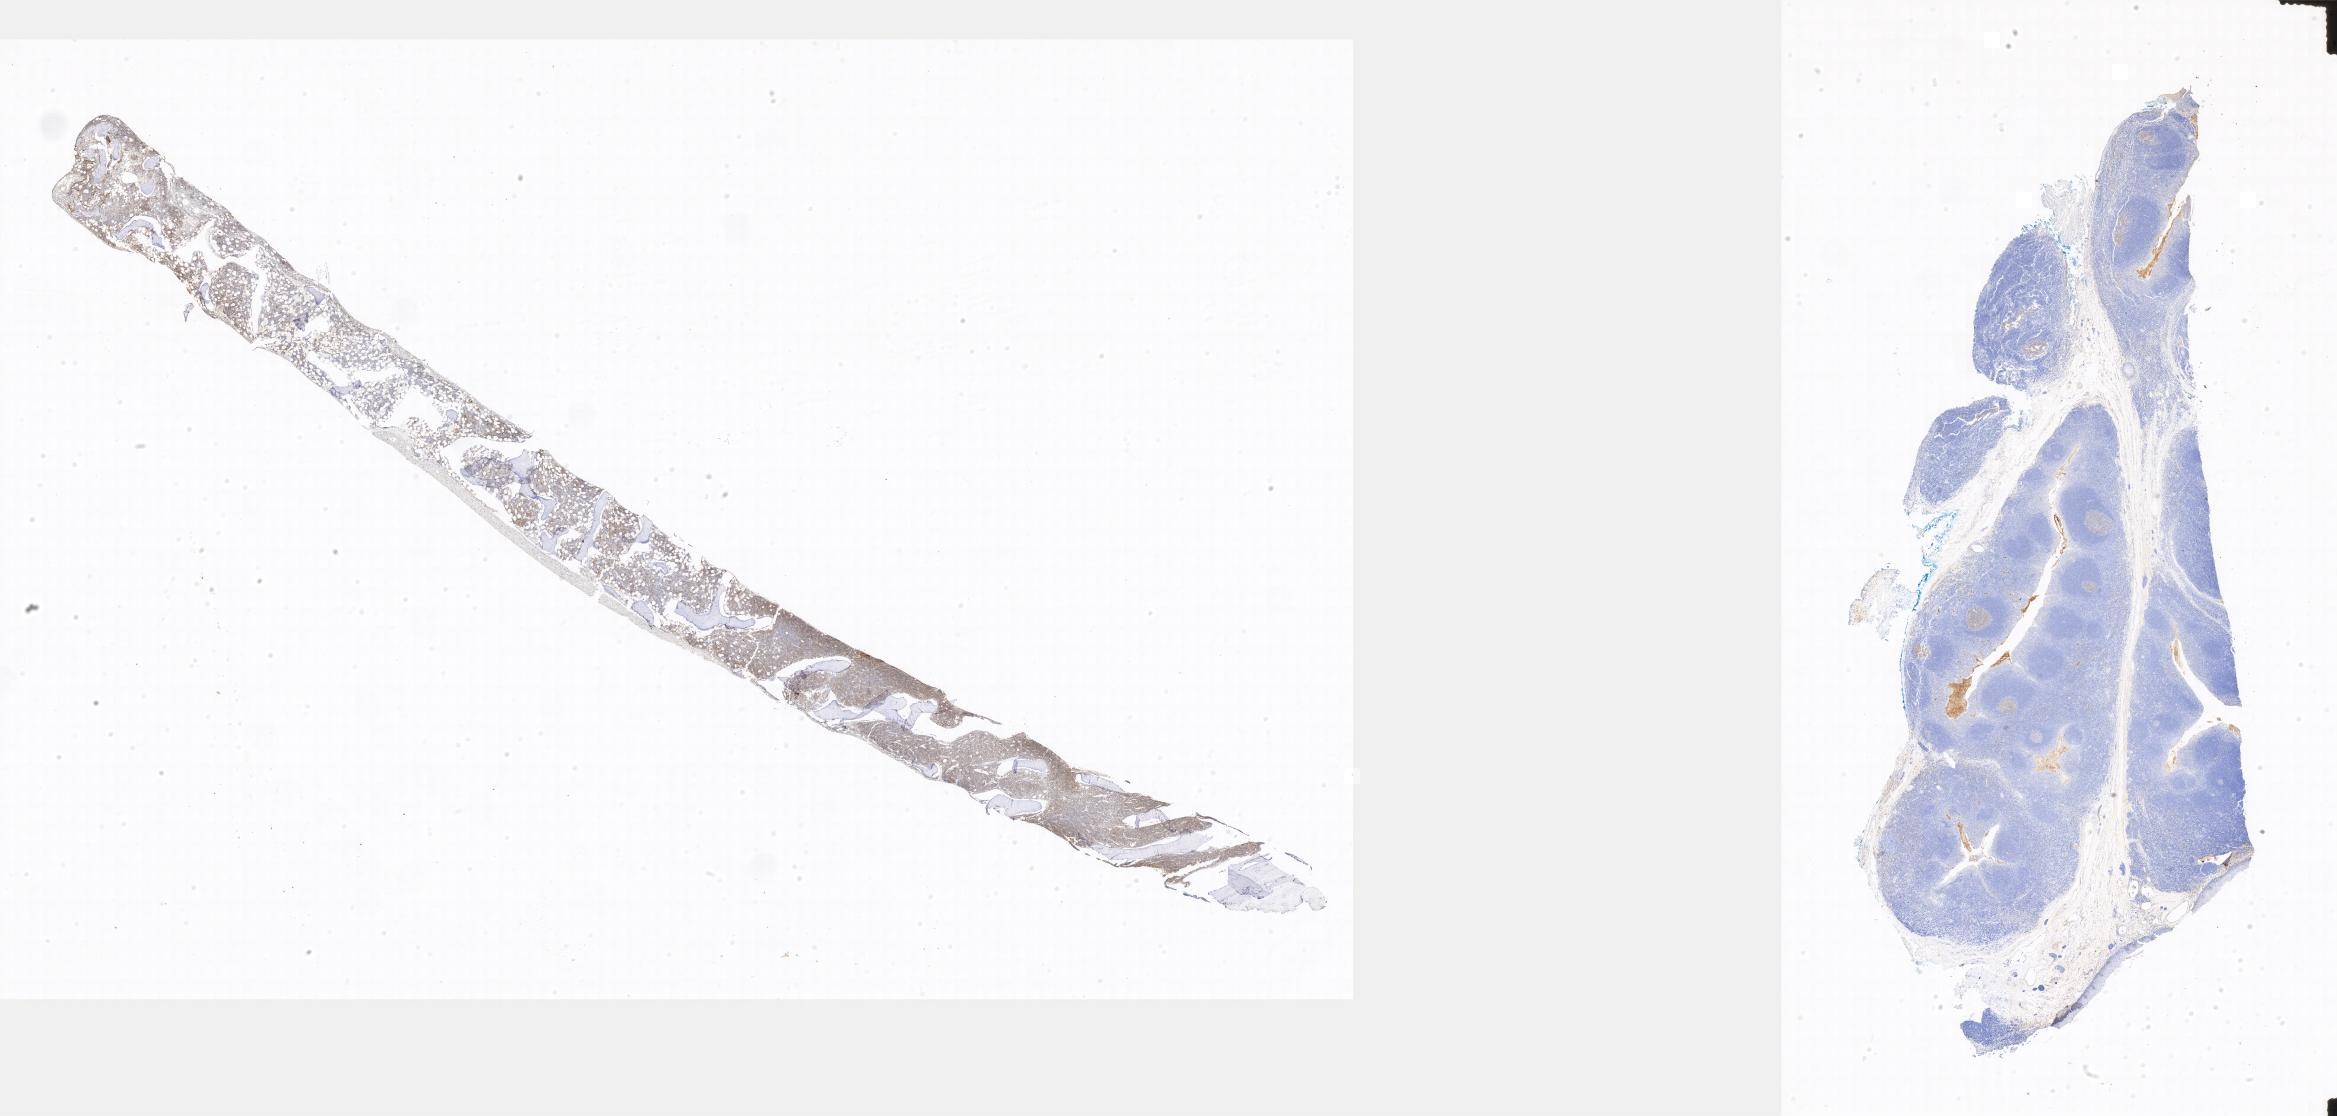
Immunohistochemistry (IHC) whole-slide image stained for CD10, low-resolution overview of the scanned area, tumor tissue. Patient: male, aged 12.
Diagnosis: Burkitt lymphoma, NOS.